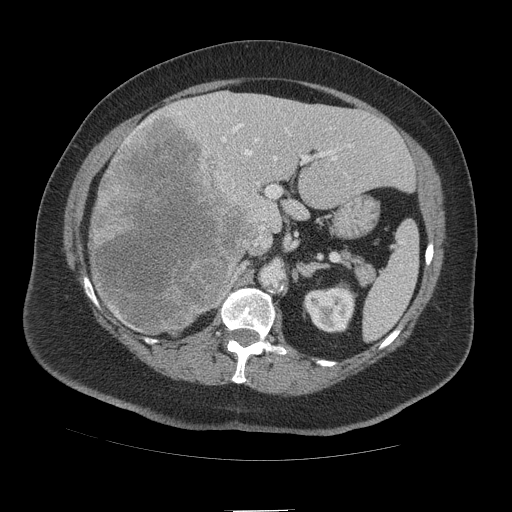
Contrast-enhanced abdominal CT (liver protocol), one axial slice. Position 60 of 109 along the scan axis. Soft-tissue window (W 400 / L 40 HU). 2.5 mm slice thickness. 512 × 512 image matrix. From the clinical record (not read from this slice): diagnosis: hepatocellular carcinoma (patient treated with transarterial chemoembolisation; whether this scan precedes or follows treatment is not stated here); TNM stage (as recorded): Stage-IVB; Child-Pugh class: A; tumour differentiation: poorly differentiated; tumour nodularity: multinodular.
Structures marked on this image (semi-automatic segmentation, software-assisted and operator-edited):
- liver parenchyma outside the tumour (the mass and vessels are separate outlines, so this box may not span the whole liver): box from (x=92, y=90) to (x=414, y=324) px
- mass: (x=88, y=113)–(x=250, y=336)
- liver vessels: (x=178, y=110)–(x=351, y=238)